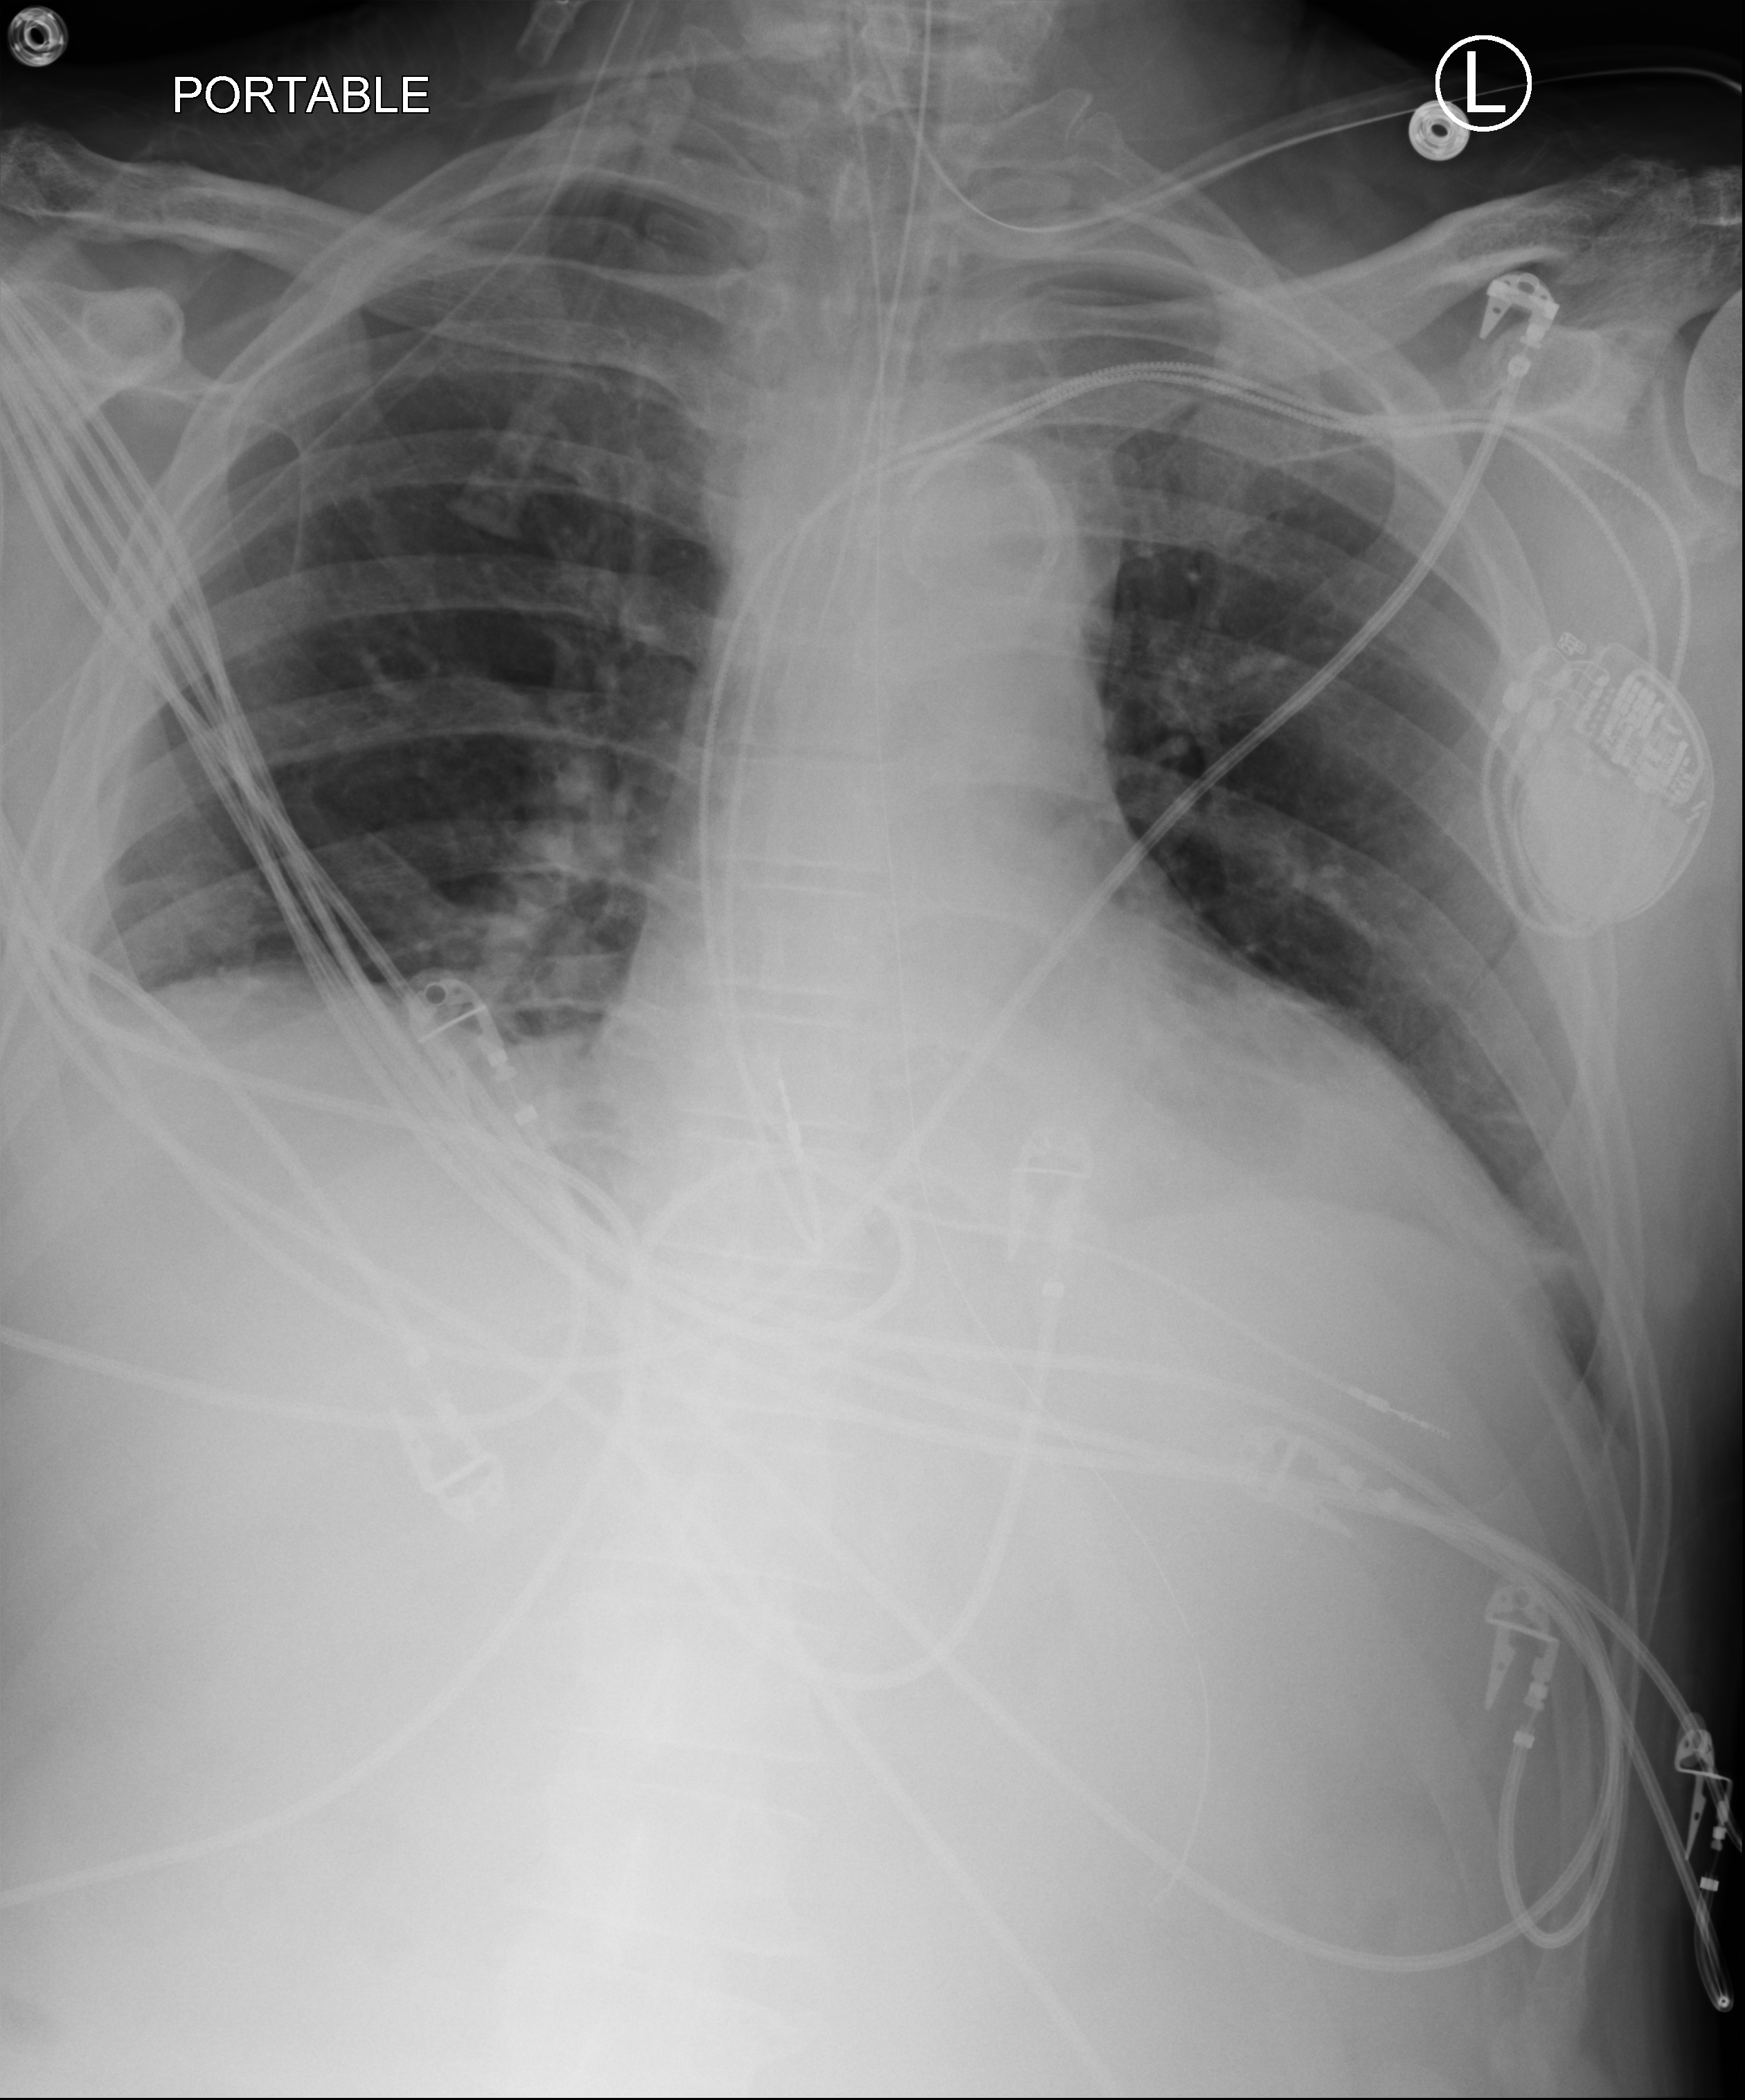
Chest X-ray (portable), anteroposterior (AP) projection. Male patient hospitalised with COVID-19, age 60–74 years.
Admission-level facts for this patient (not findings on this image; timing relative to this image not recorded): admitted to intensive care during this hospital stay: yes.